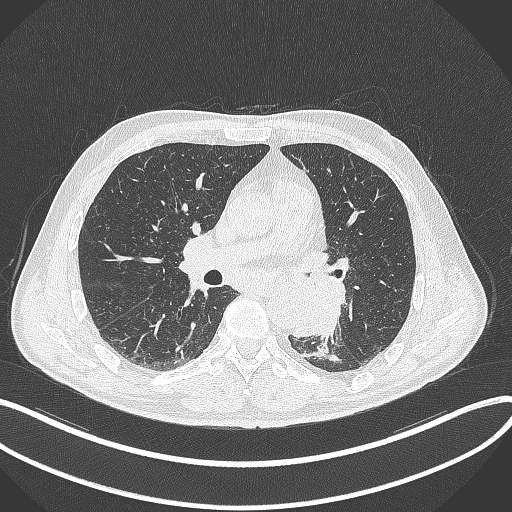
Chest CT, one axial slice. Position 181 of 329 along the scan axis. Reconstruction kernel B70f. 120 kVp. Lung window (W 1500 / L -600 HU). 512 × 512 image matrix, field of view 400 × 400 mm. Male patient, age 59 years. Case-level facts recorded for this patient, not image findings: clinical TNM (as recorded): T2a N2 M0.
Annotated regions visible in this slice (bounding box drawn by a radiologist):
- lung tumour (recorded histology: squamous cell carcinoma): bounding box (x1, y1, x2, y2) in pixels: (286, 273, 349, 342)